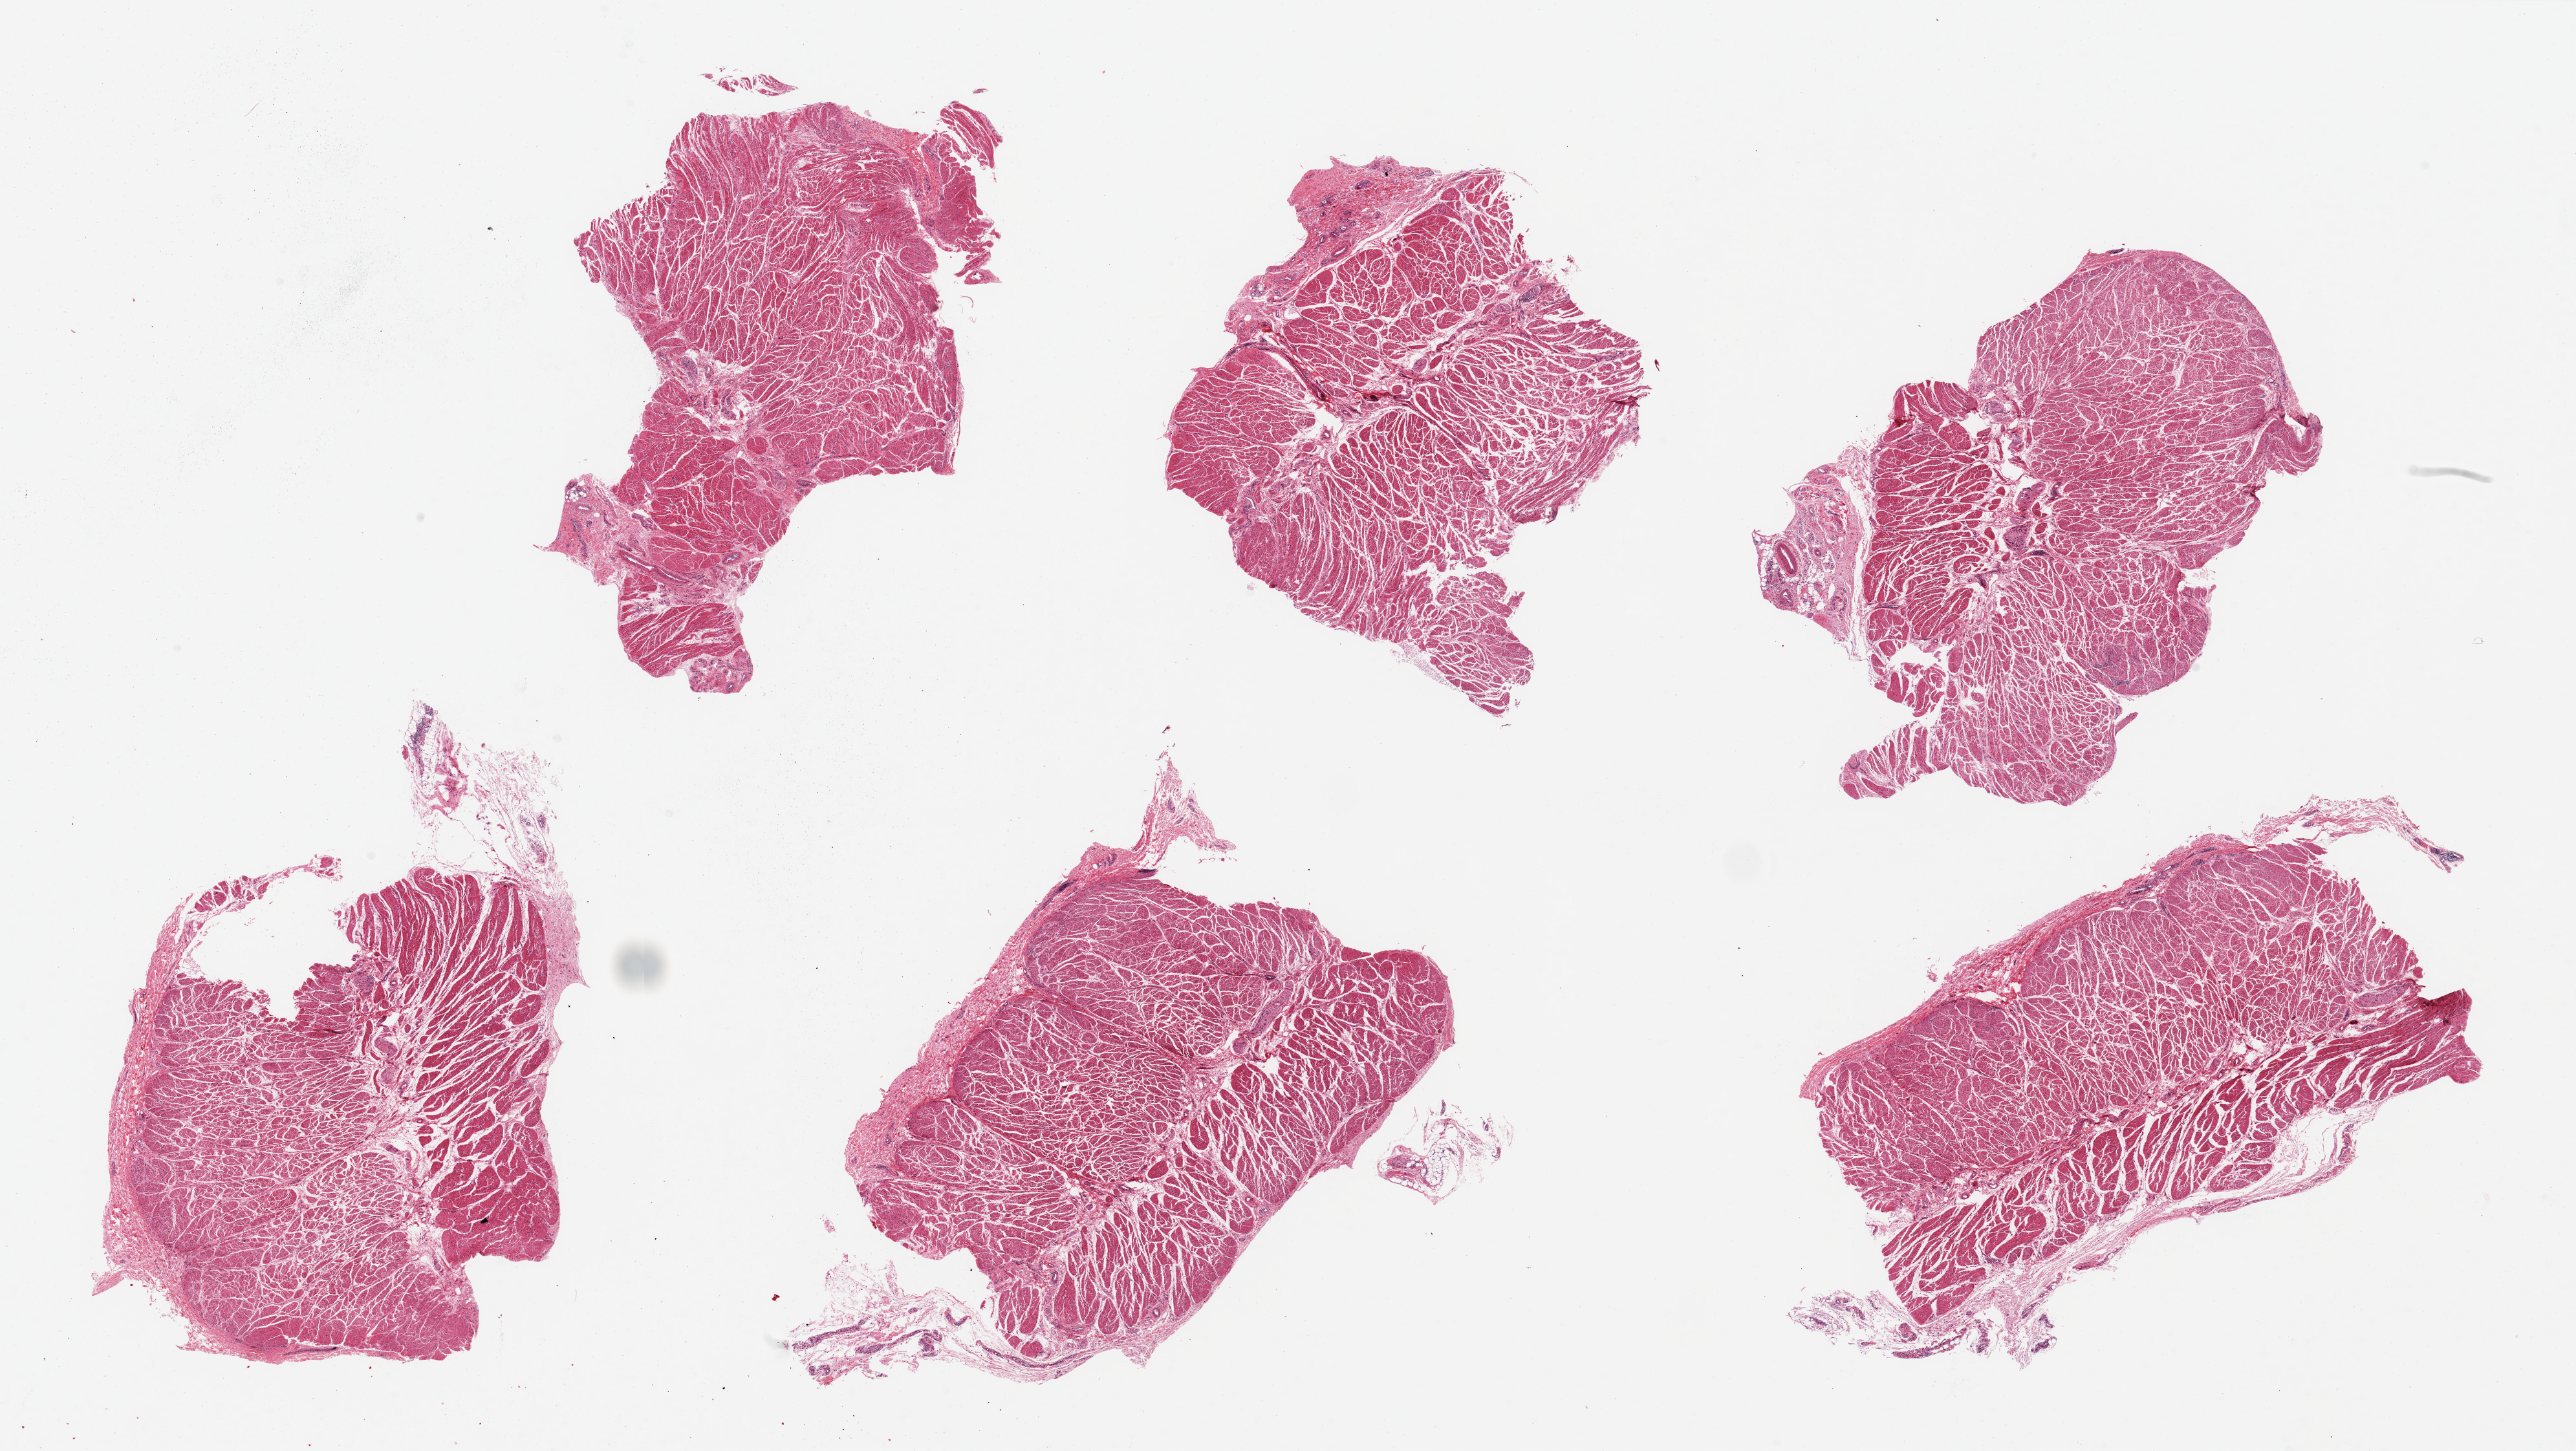
Whole-slide image, hematoxylin and eosin (H&E) stain, brightfield, a low-resolution overview of the entire scanned area, about 31.5 x 17.7 mm (acquisition: 20x scan), PAXgene-fixed paraffin-embedded (PFPE) section, sampled site (target tissue): esophageal muscle, donor tissue sample. Donor: male.
- review note (as recorded): 6 pieces up to 8x4 mm